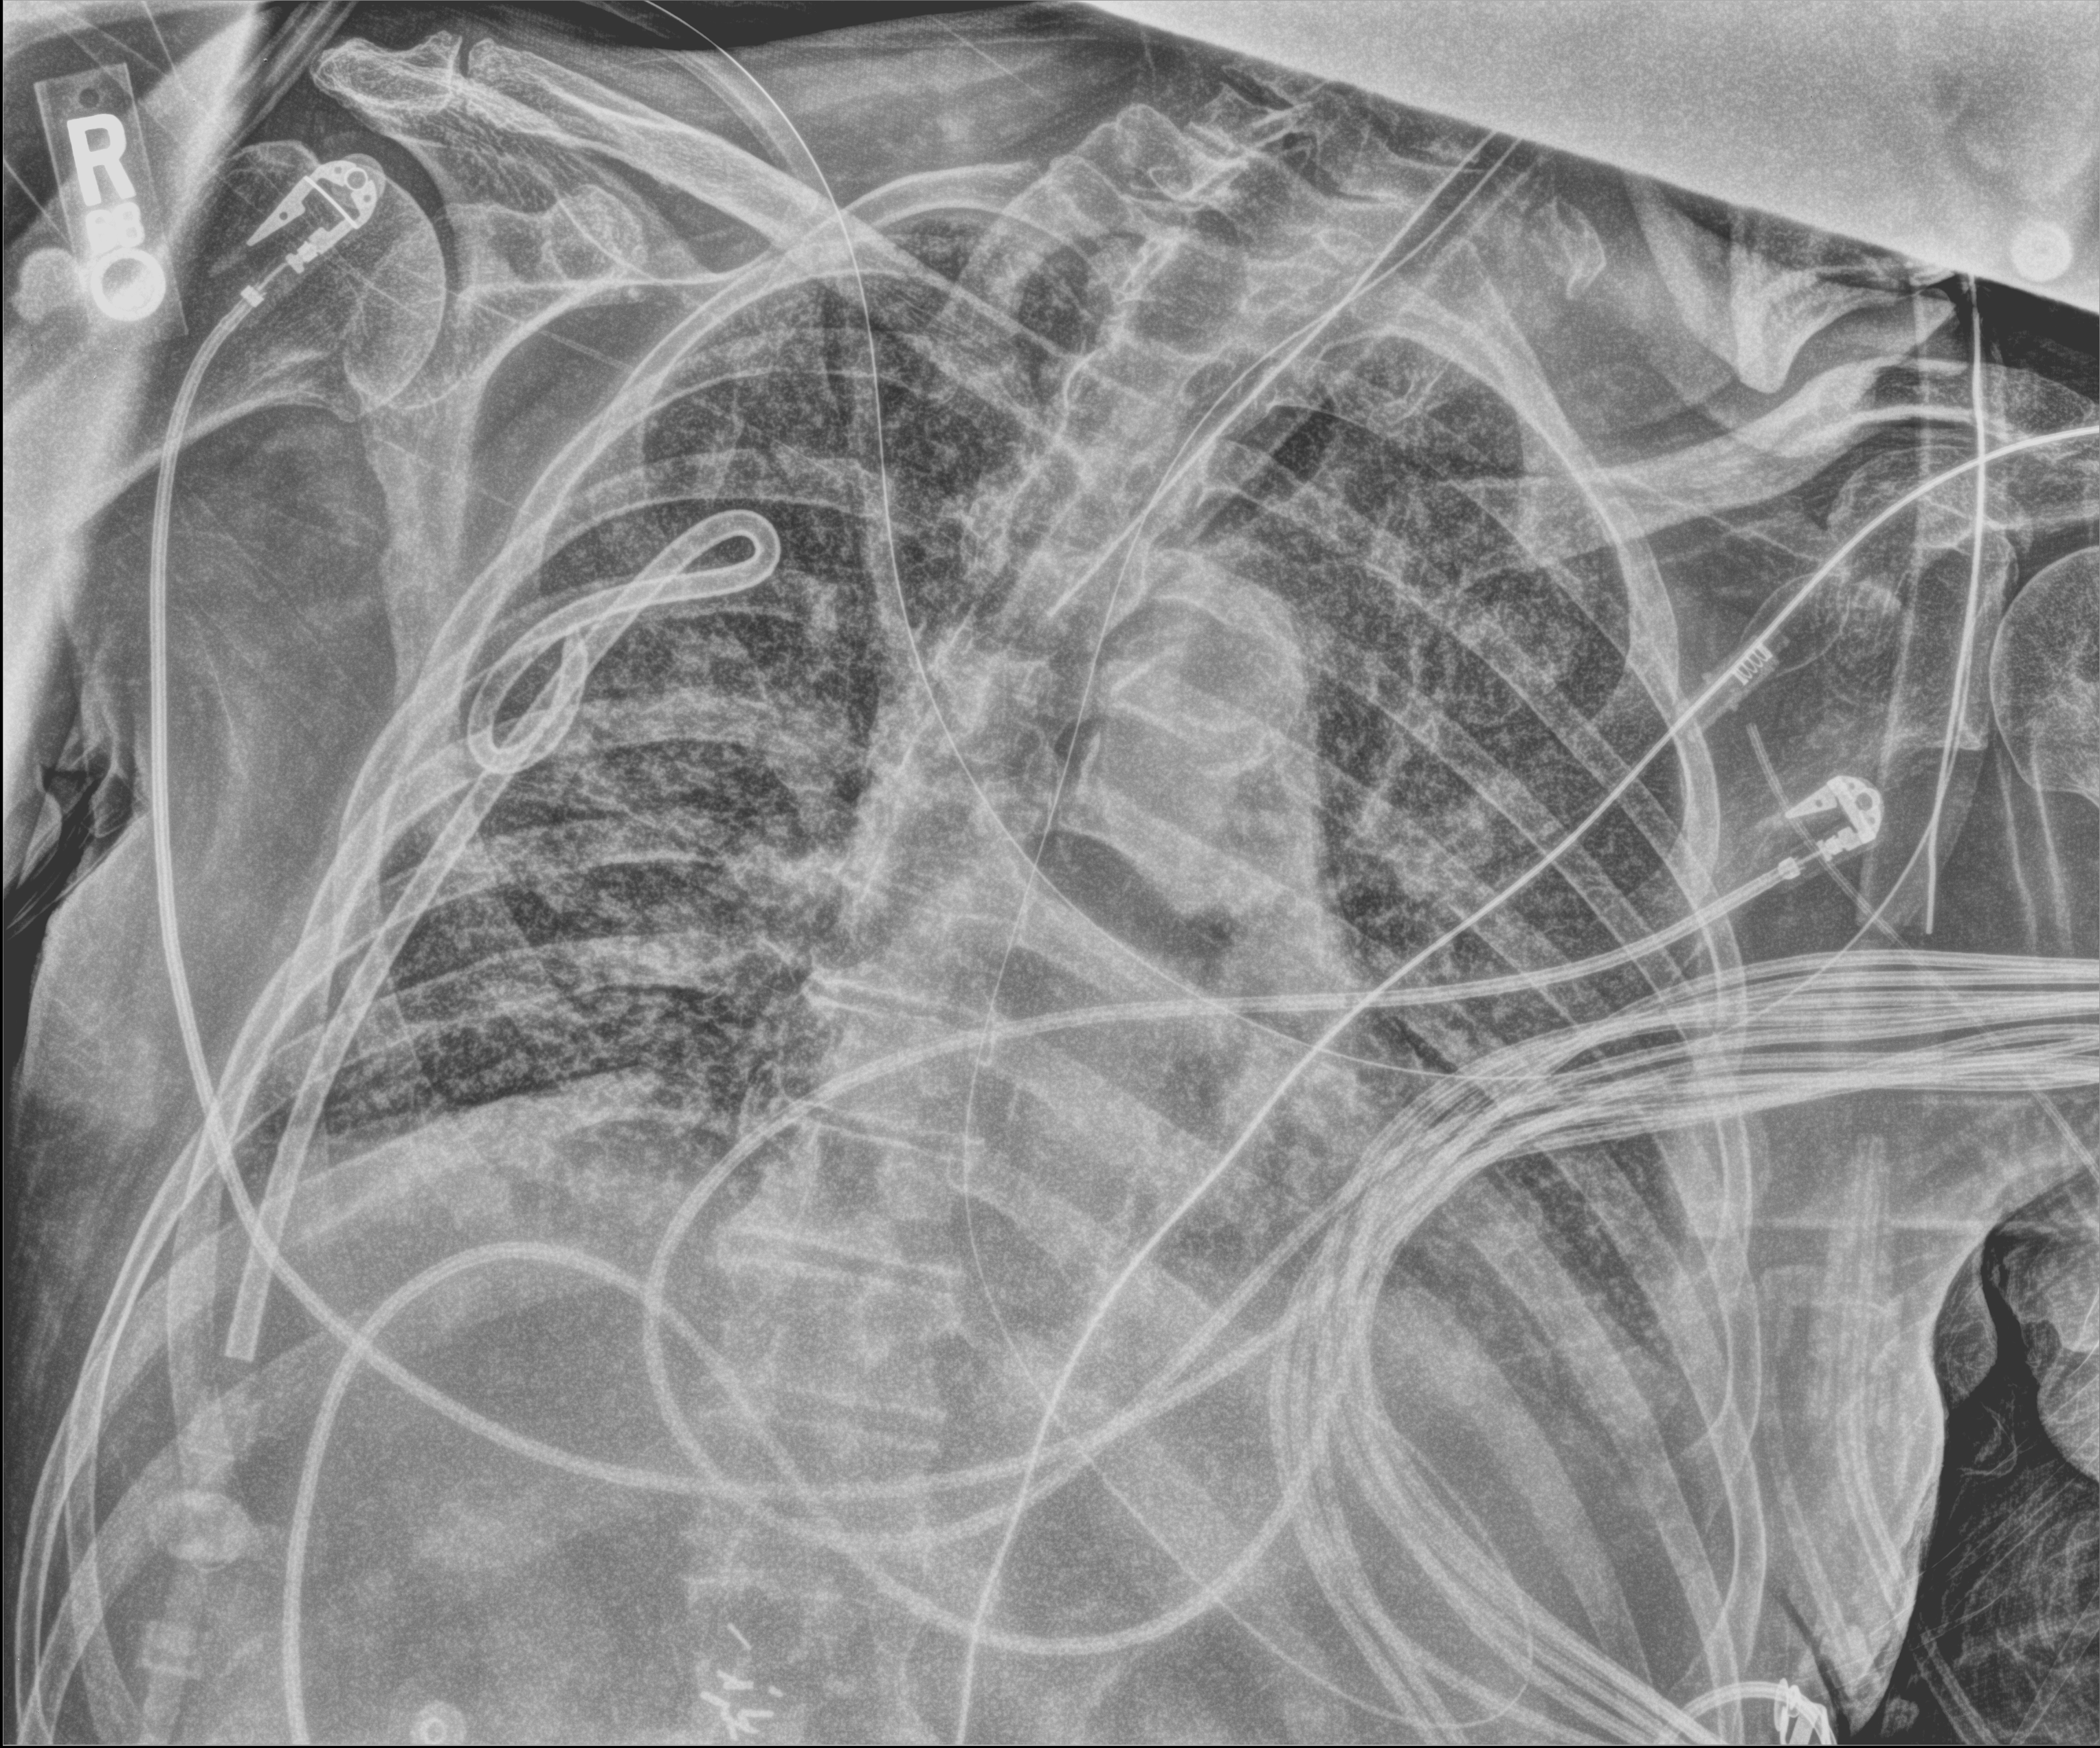
Portable chest radiograph, anteroposterior (AP) projection. Male patient hospitalised with COVID-19, age 75–90 years.
Admission-level facts for this patient (not findings on this image; timing relative to this image not recorded): admitted to intensive care during this hospital stay: yes; other chronic lung disease (admission record): no; mechanically ventilated during this hospital stay: yes.